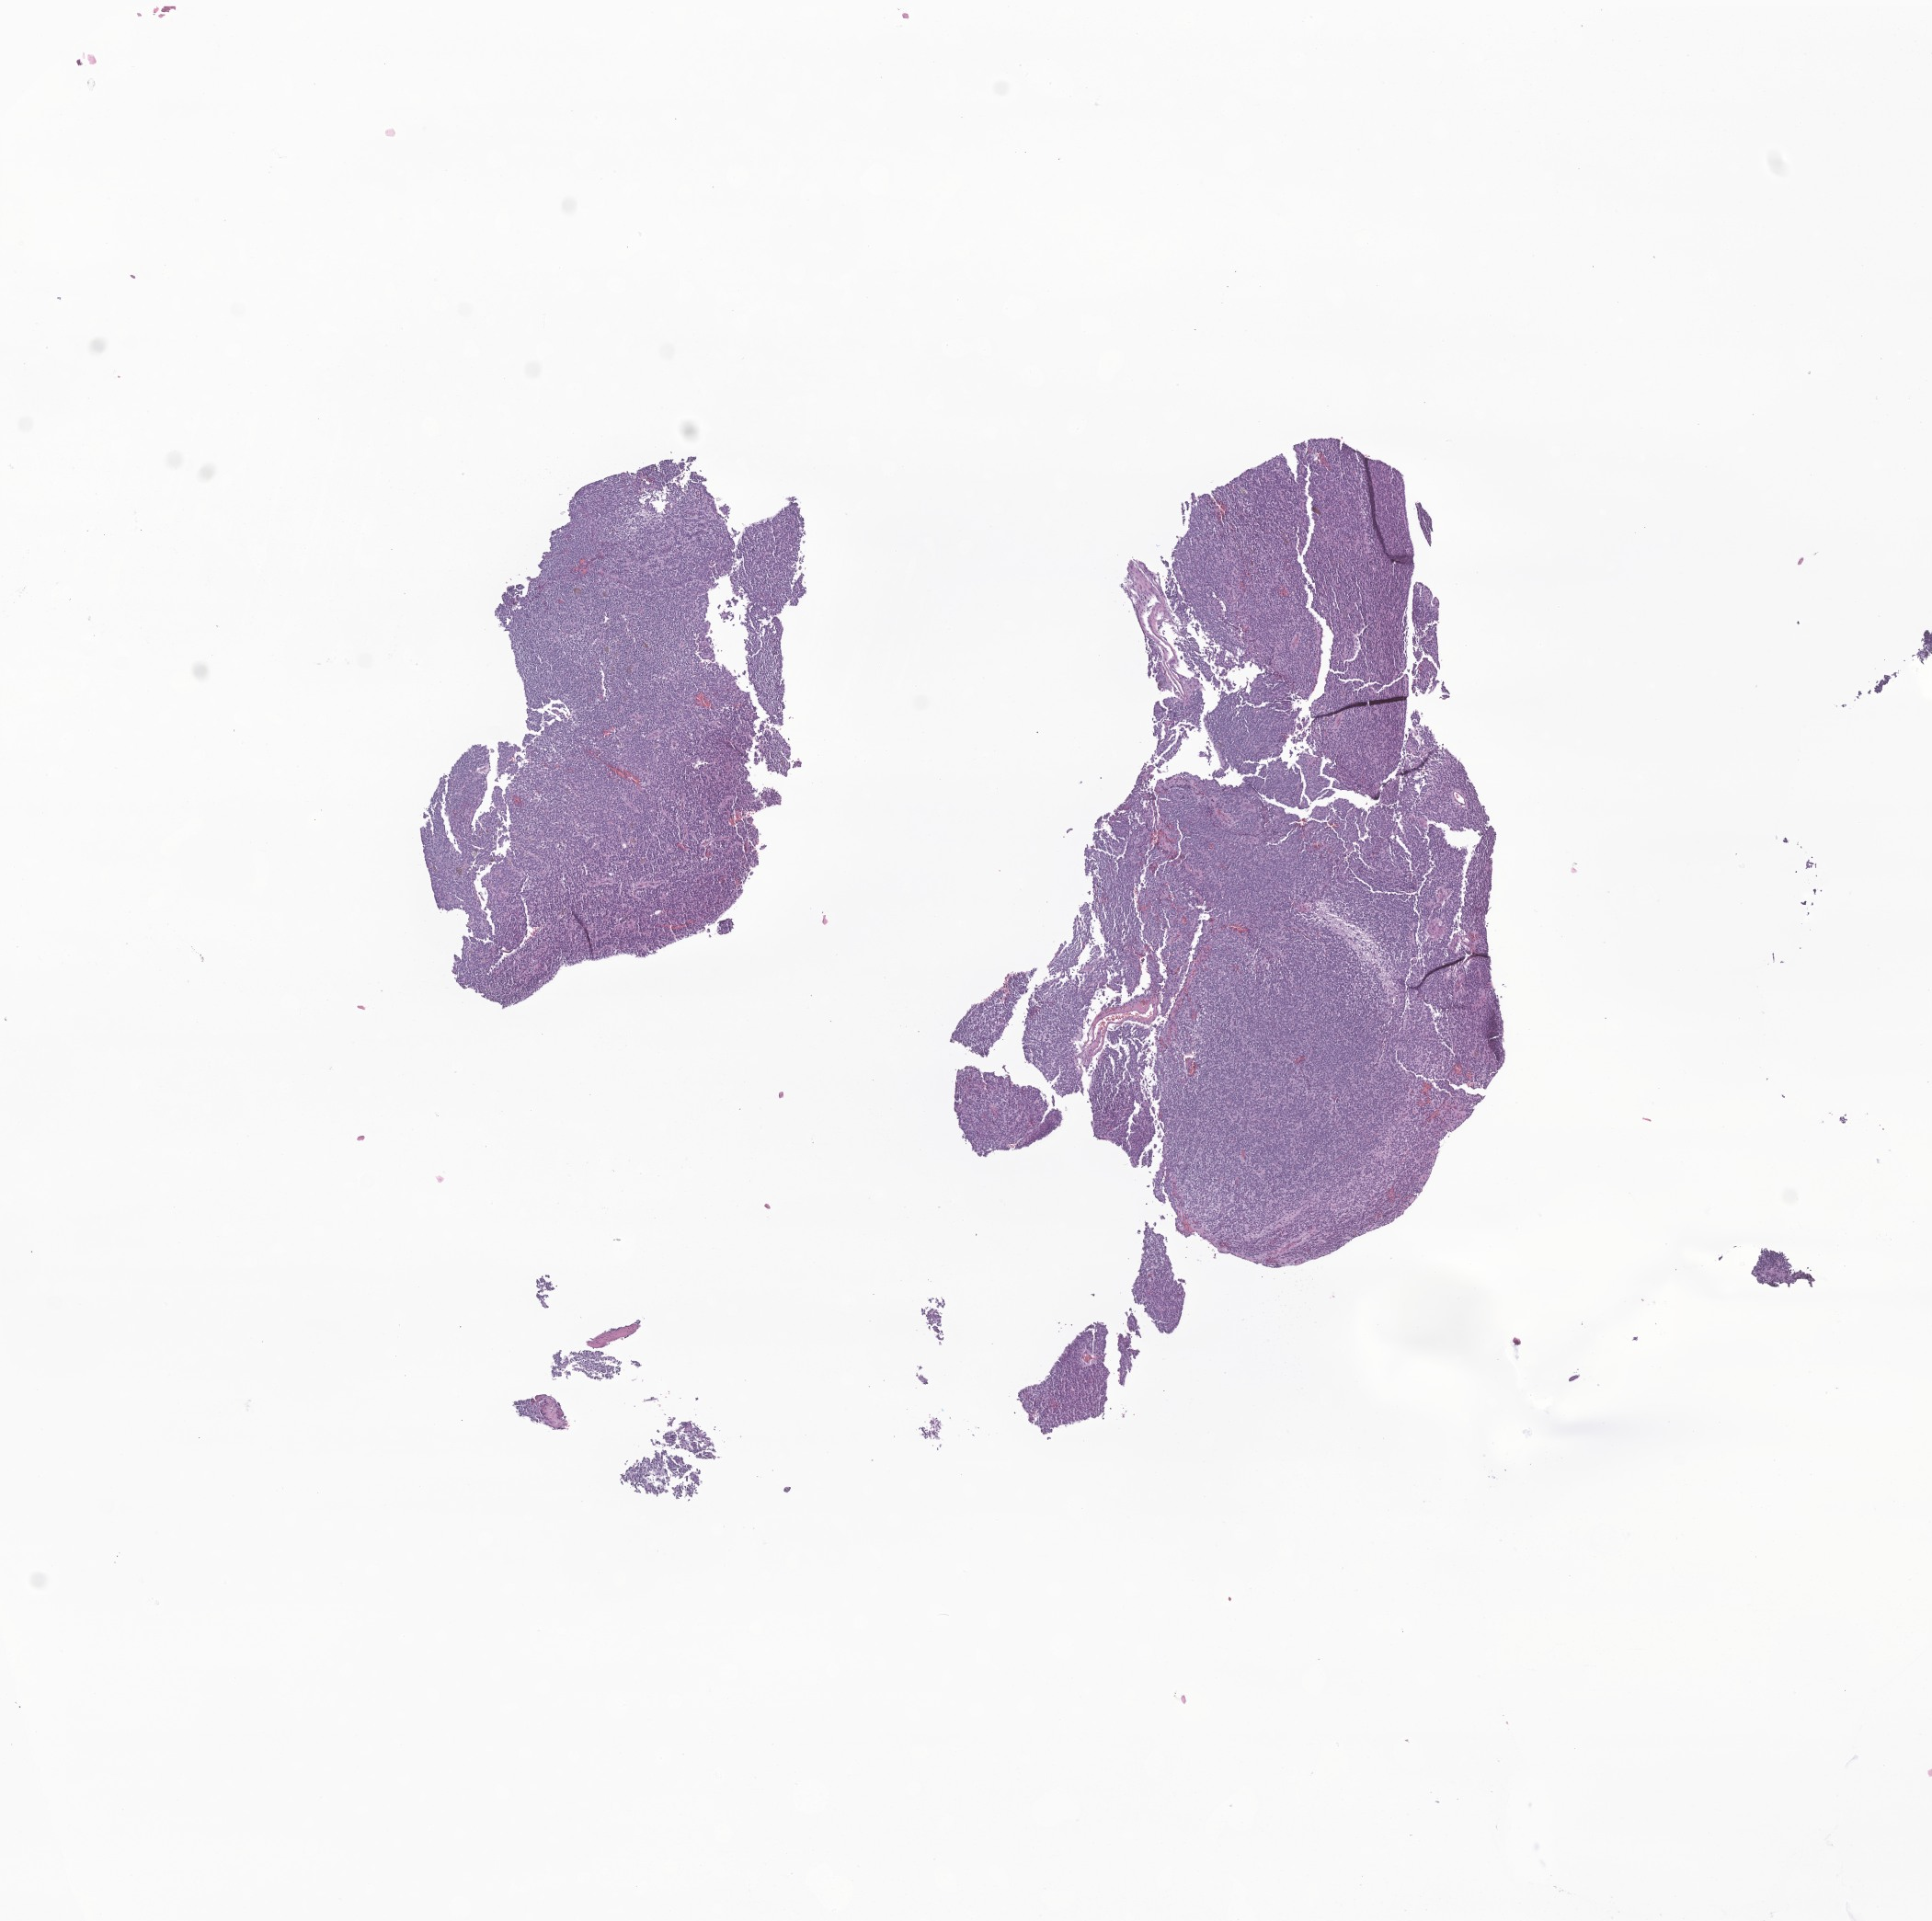
Whole-slide image, H&E stain of tumor tissue from the brain — whole scanned area (about 8.9 x 8.8 mm) shown as a low-resolution overview. FFPE section. Male patient, age 231 months.
Diagnosis: Central neurocytoma.